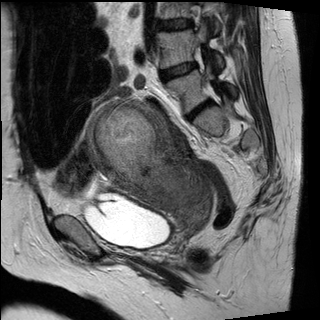
Pelvic MRI for cervical cancer, one sagittal slice. Position 18 of 30 along the scan axis. T2-weighted. 1.5 T. TE 89 ms, TR 2930 ms. 4 mm slice thickness. 320 × 320 image matrix, field of view 260 × 260 mm. Patient: female, 62 years.
Structures marked on this image (expert manual segmentation):
- uterus and cervix: box from (x=84, y=97) to (x=212, y=232) px